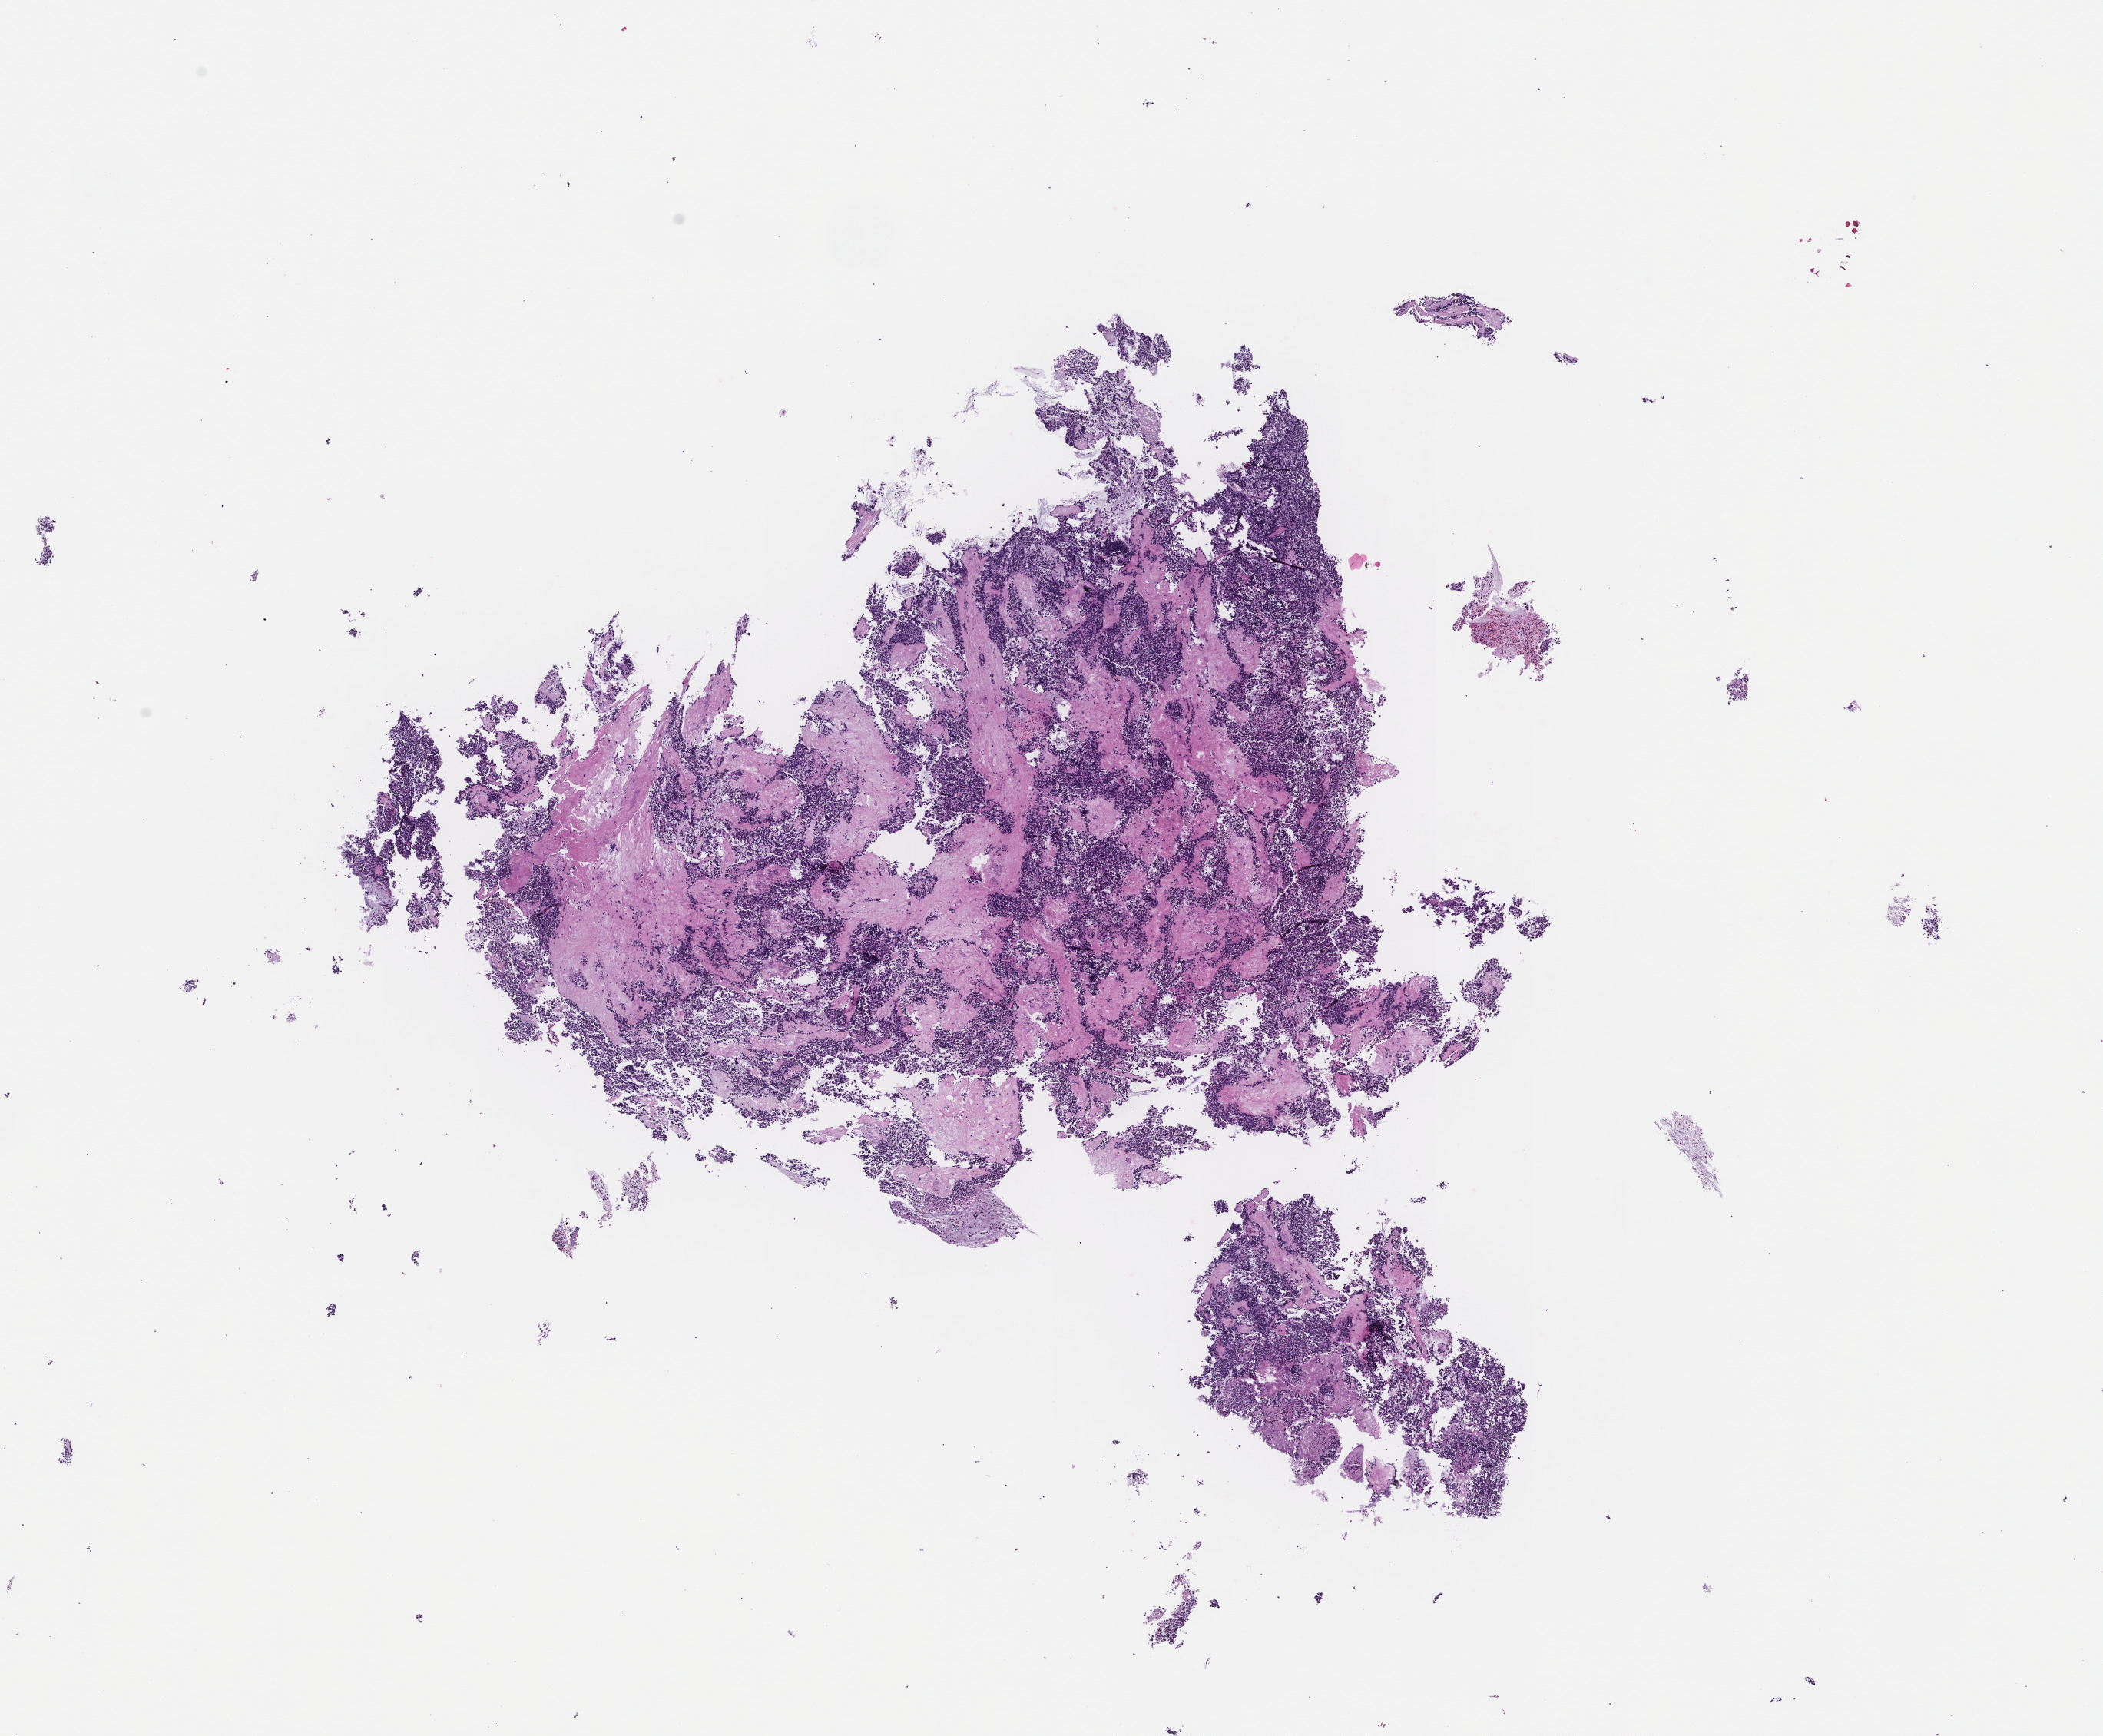
Hematoxylin and eosin (H&E) whole-slide image, whole scanned area (about 11.1 x 9.1 mm) shown as a low-resolution overview, FFPE section, site: lung, archival tissue. Patient: male.
This section: primary tumour tissue. Diagnosis: Small Cell Lung Carcinoma.